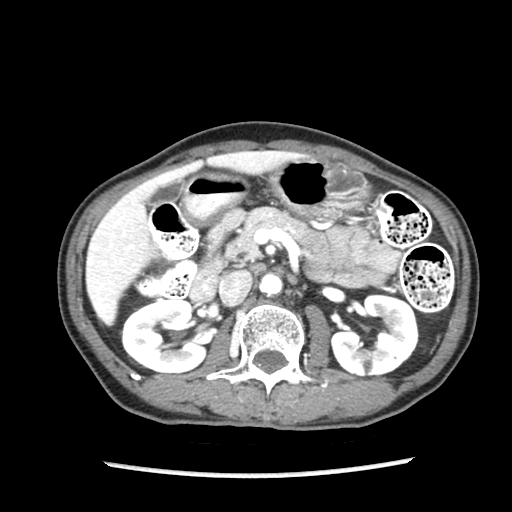
Contrast-enhanced abdominal CT (liver protocol), one axial slice; slice 42 of 87 in the series (ordered by position); reconstruction kernel STANDARD; soft-tissue window (W 400 / L 40 HU); 2.5 mm slice thickness; 512 × 512 image matrix, field of view 300 × 300 mm. Case-level facts recorded for this patient, not image findings: diagnosis: hepatocellular carcinoma (patient treated with transarterial chemoembolisation; whether this scan precedes or follows treatment is not stated here); TNM stage (as recorded): Stage-IIIB; Child-Pugh class: A; tumour differentiation: well differentiated.
Outlined on this slice (semi-automatically segmented with operator editing):
- liver parenchyma outside the tumour (the mass and vessels are separate outlines, so this box may not span the whole liver): bounding box <86,152,252,324> (left, top, right, bottom; pixels)
- liver vessels: <89,176,169,312>